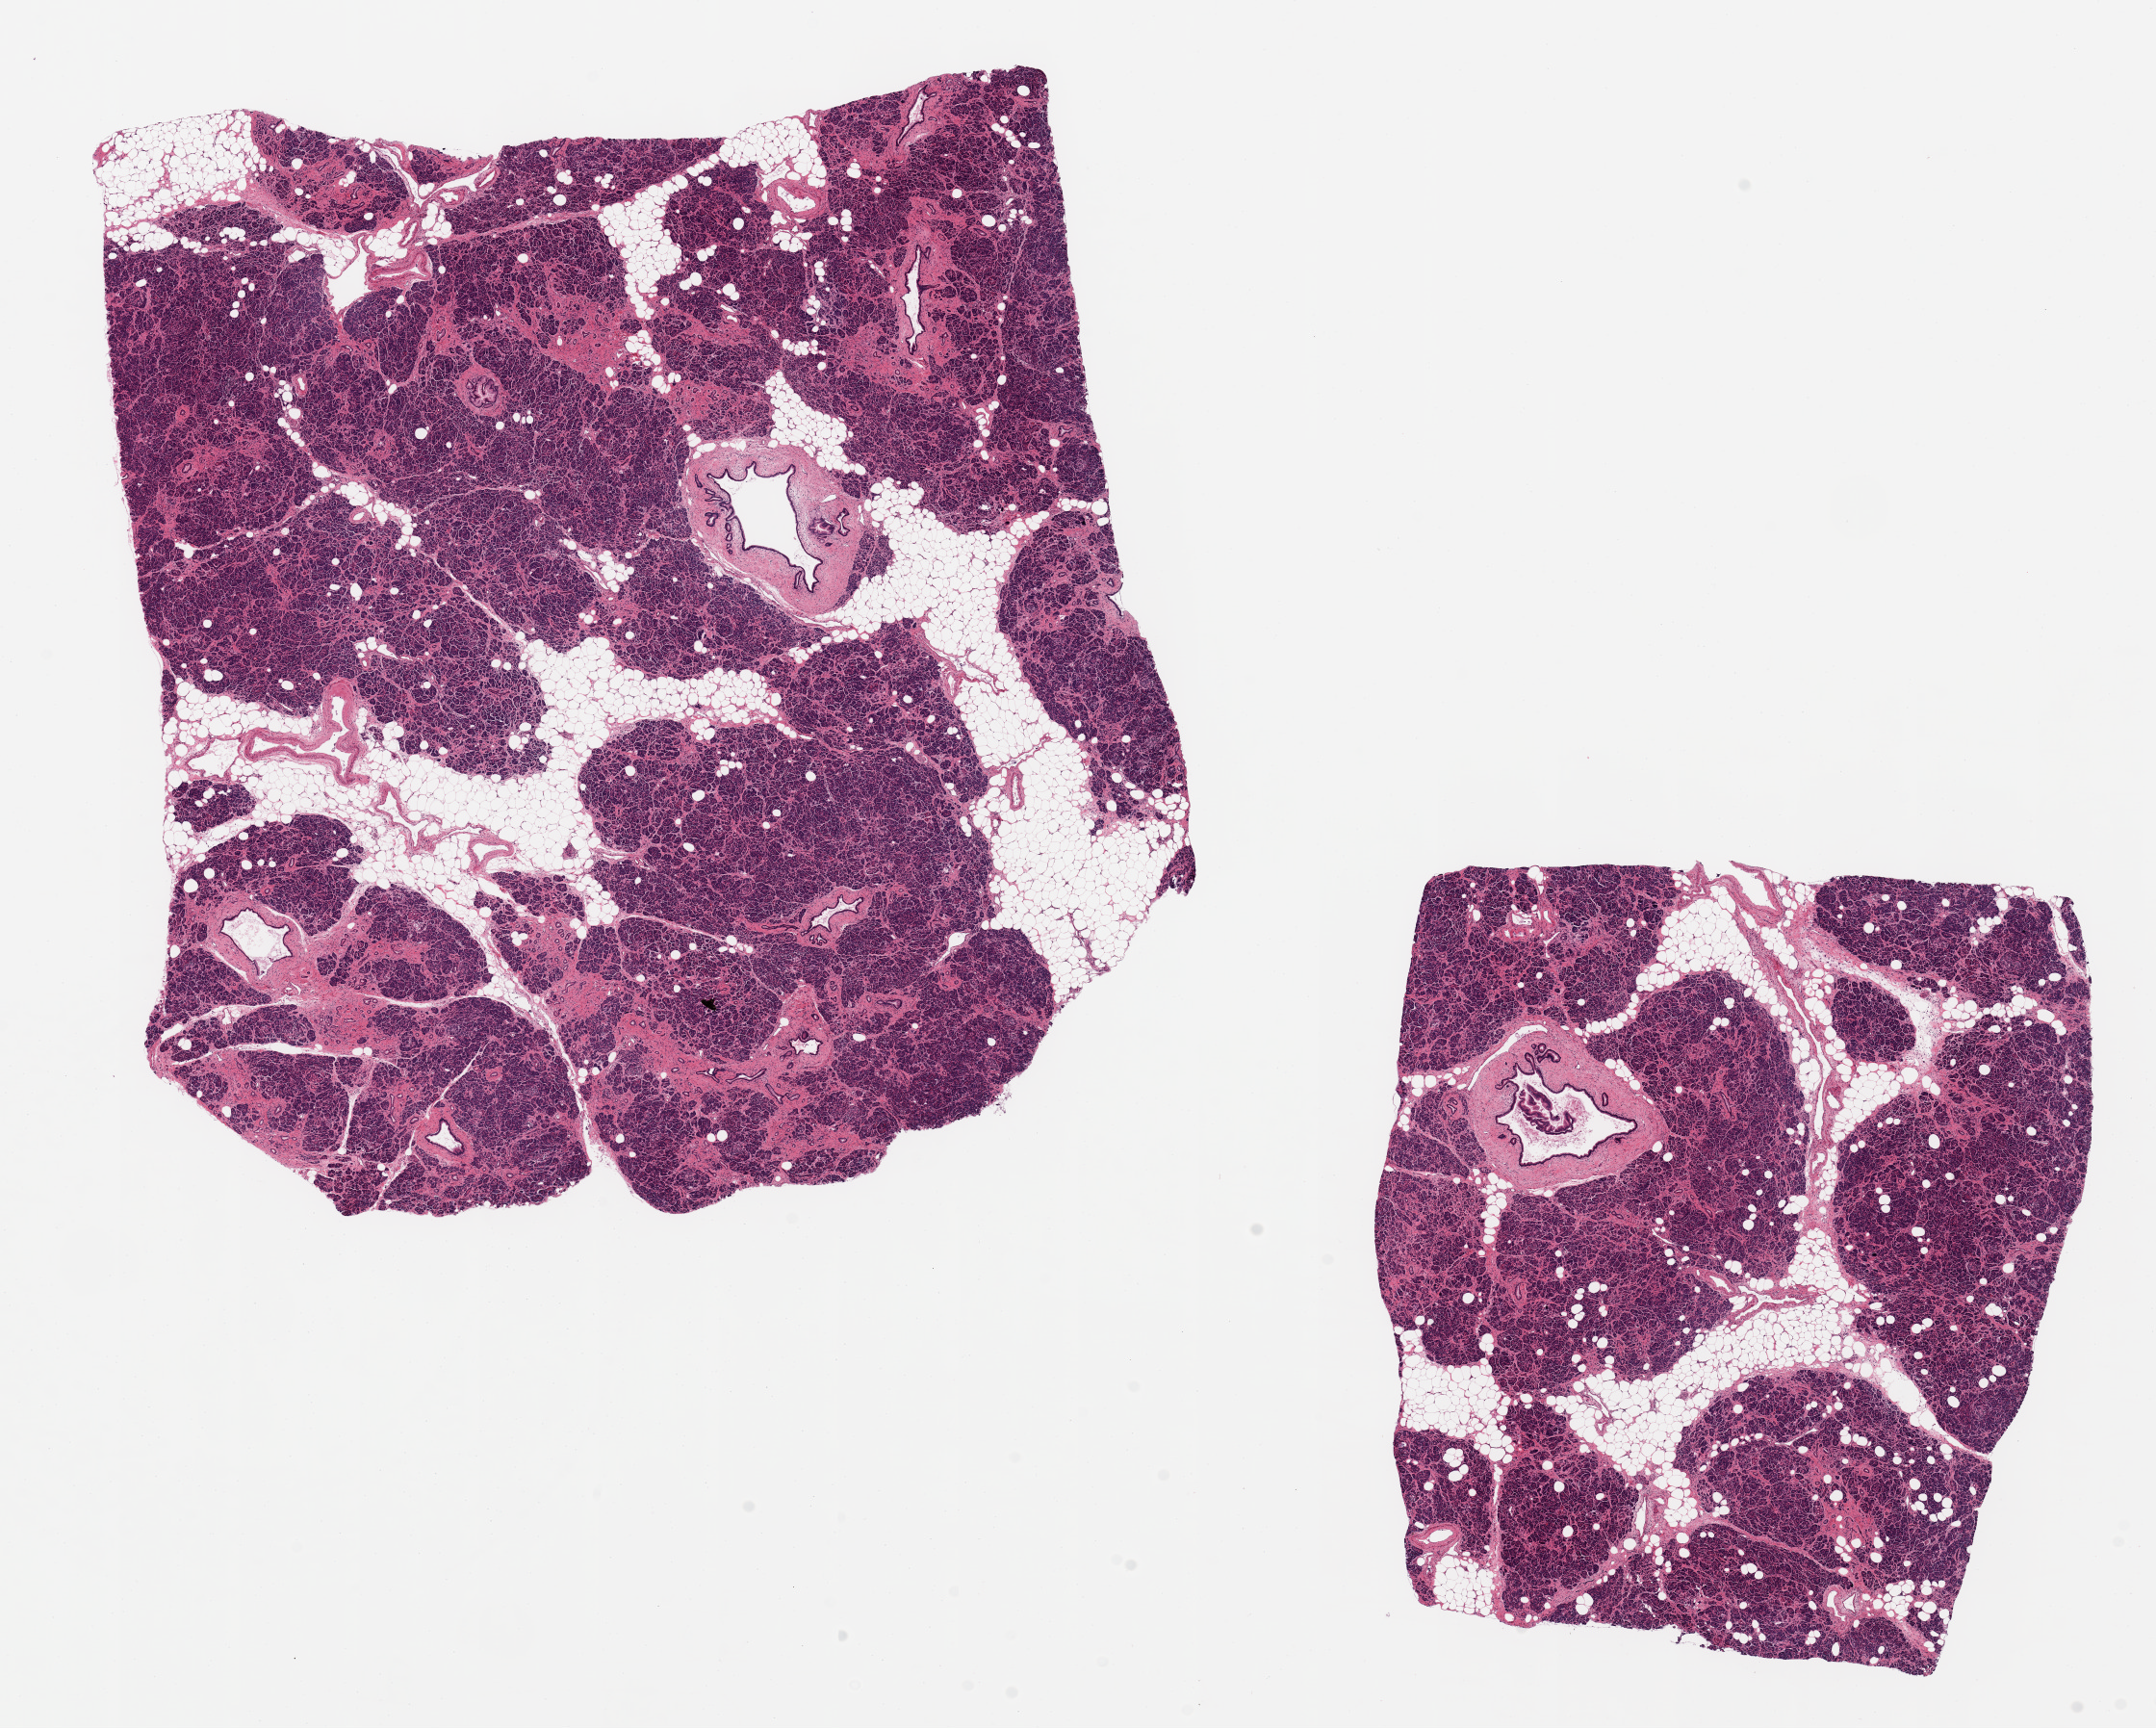
Whole-slide image, H&E stain — a low-resolution overview of the entire scanned area, about 17.7 x 14.2 mm (from a 20x scan); PAXgene-fixed, paraffin-embedded tissue; target tissue: pancreas; donor tissue sample. Donor: male.
* reviewer comment on this tissue sample: 2 ~7.5x6.5mm aliquots, ~30% interstitial fat, reduced numbers of Islets